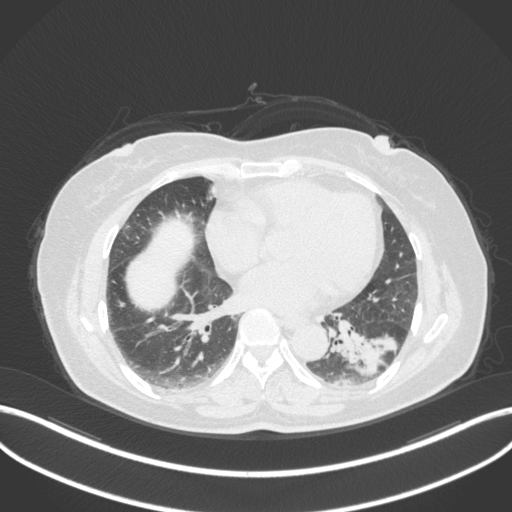
Chest CT, one axial slice; position 153 of 307 along the scan axis; reconstruction kernel B31f; lung window (W 1500 / L -600 HU); 1 mm slice thickness; 512 × 512 image matrix. Patient: female, 59 years. From the clinical record (not read from this slice): clinical TNM (as recorded): T2a N0 M0.
Annotated regions visible in this slice (rectangle marked by the reading radiologist):
- lung tumour (recorded histology: adenocarcinoma): bounding box <332,319,402,381> (left, top, right, bottom; pixels)